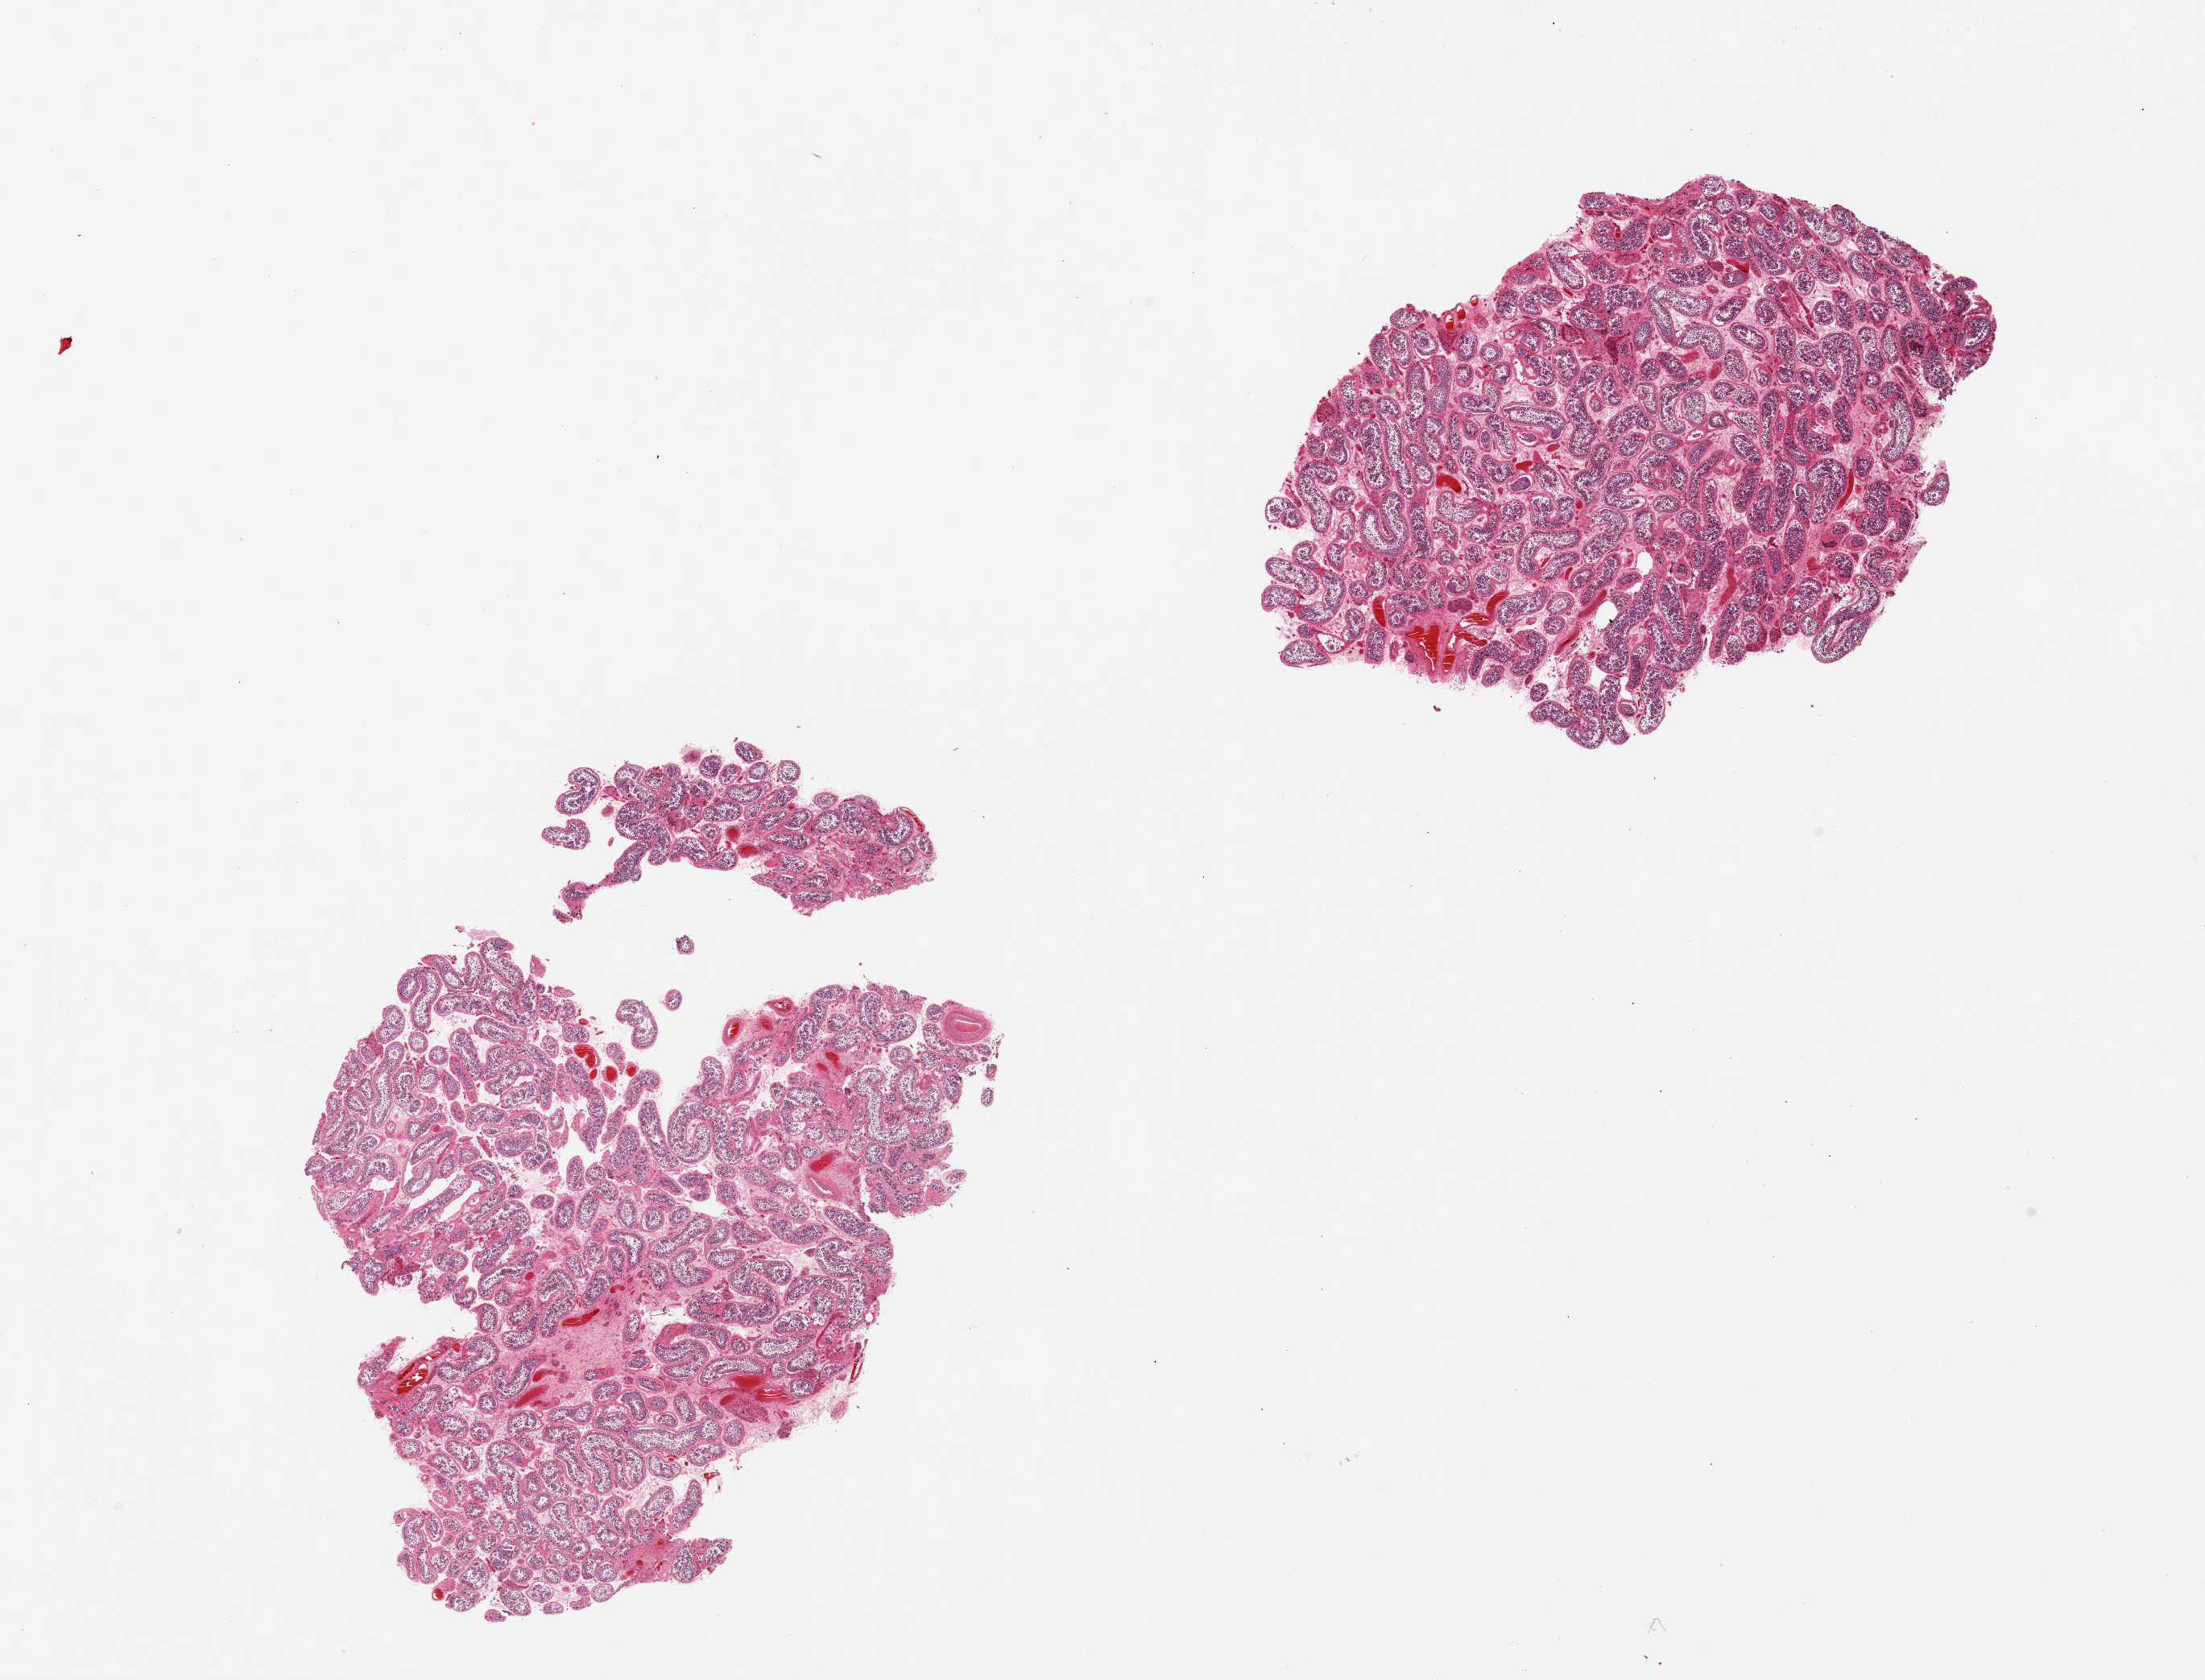
Whole-slide image, haematoxylin and eosin stain, low-resolution overview of the scanned area, about 21.7 x 16.5 mm (acquisition: 20x scan), PAXgene-fixed paraffin-embedded (PFPE) section, target tissue: testis, tissue donor sample.
Review note (as recorded): 2 pieces; spermatogenesis.